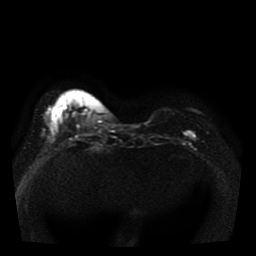
Breast MRI, one axial slice; slice 12 of 41 in the series (ordered by position); diffusion-weighted series; image 2 of 4 stored at this slice position (different b-values; order by instance number); 1.5 T; 5 mm slice thickness; 256 × 256 image matrix, field of view 330 × 330 mm. Female patient.
Structures marked on this image (manually delineated by an expert):
- tumour on diffusion-weighted imaging: bounding box [x1, y1, x2, y2] px = [185, 131, 195, 137]